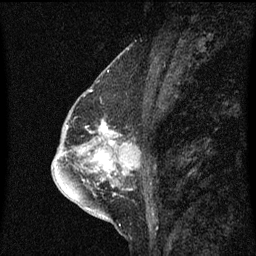
Breast MRI (dynamic contrast-enhanced), one sagittal slice; position 32 of 60 along the scan axis; dynamic contrast-enhanced series, image 2 of 3 at this slice position (ordered by acquisition); 1.5 T; TE 4.2 ms, TR 8.4 ms; 2 mm slice thickness; 256 × 256 image matrix, field of view 200 × 200 mm. Patient: female, 57 years. Case-level facts recorded for this patient, not image findings: setting: breast cancer imaged before/during neoadjuvant chemotherapy; receptor status: HR-positive, HER2-negative.
Annotated regions visible in this slice (semi-automatically segmented with operator editing):
- analysis volume of interest (the breast-tissue region the enhancement analysis was run in; not a lesion): box from (x=88, y=120) to (x=128, y=145) px
- tumour enhancement mask (voxels above the 70 % enhancement threshold inside the analysis volume of interest): (x=101, y=122)–(x=115, y=145)